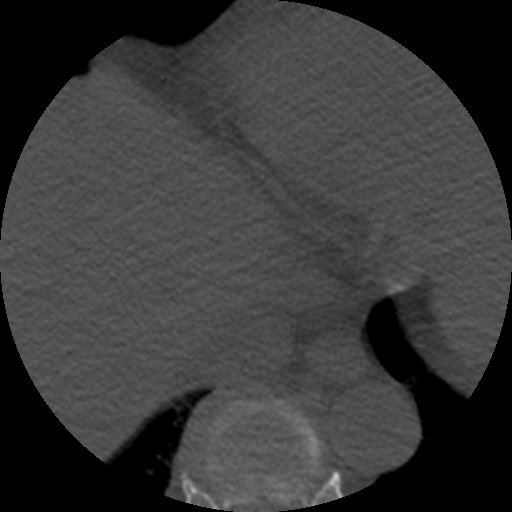
CT including the spine, one axial slice. Slice 301 of 508 in the series (ordered by position). Bone window (W 1800 / L 400 HU). 1.25 mm slice thickness. 512 × 512 image matrix. Patient age 57 years. Case-level facts recorded for this patient, not image findings: primary cancer: prostate.
Outlined on this slice (semi-automatic segmentation, software-assisted and operator-edited):
- T8 vertebra: bounding box <208,399,321,512> (left, top, right, bottom; pixels)
- T9 vertebra: <305,498,307,501>